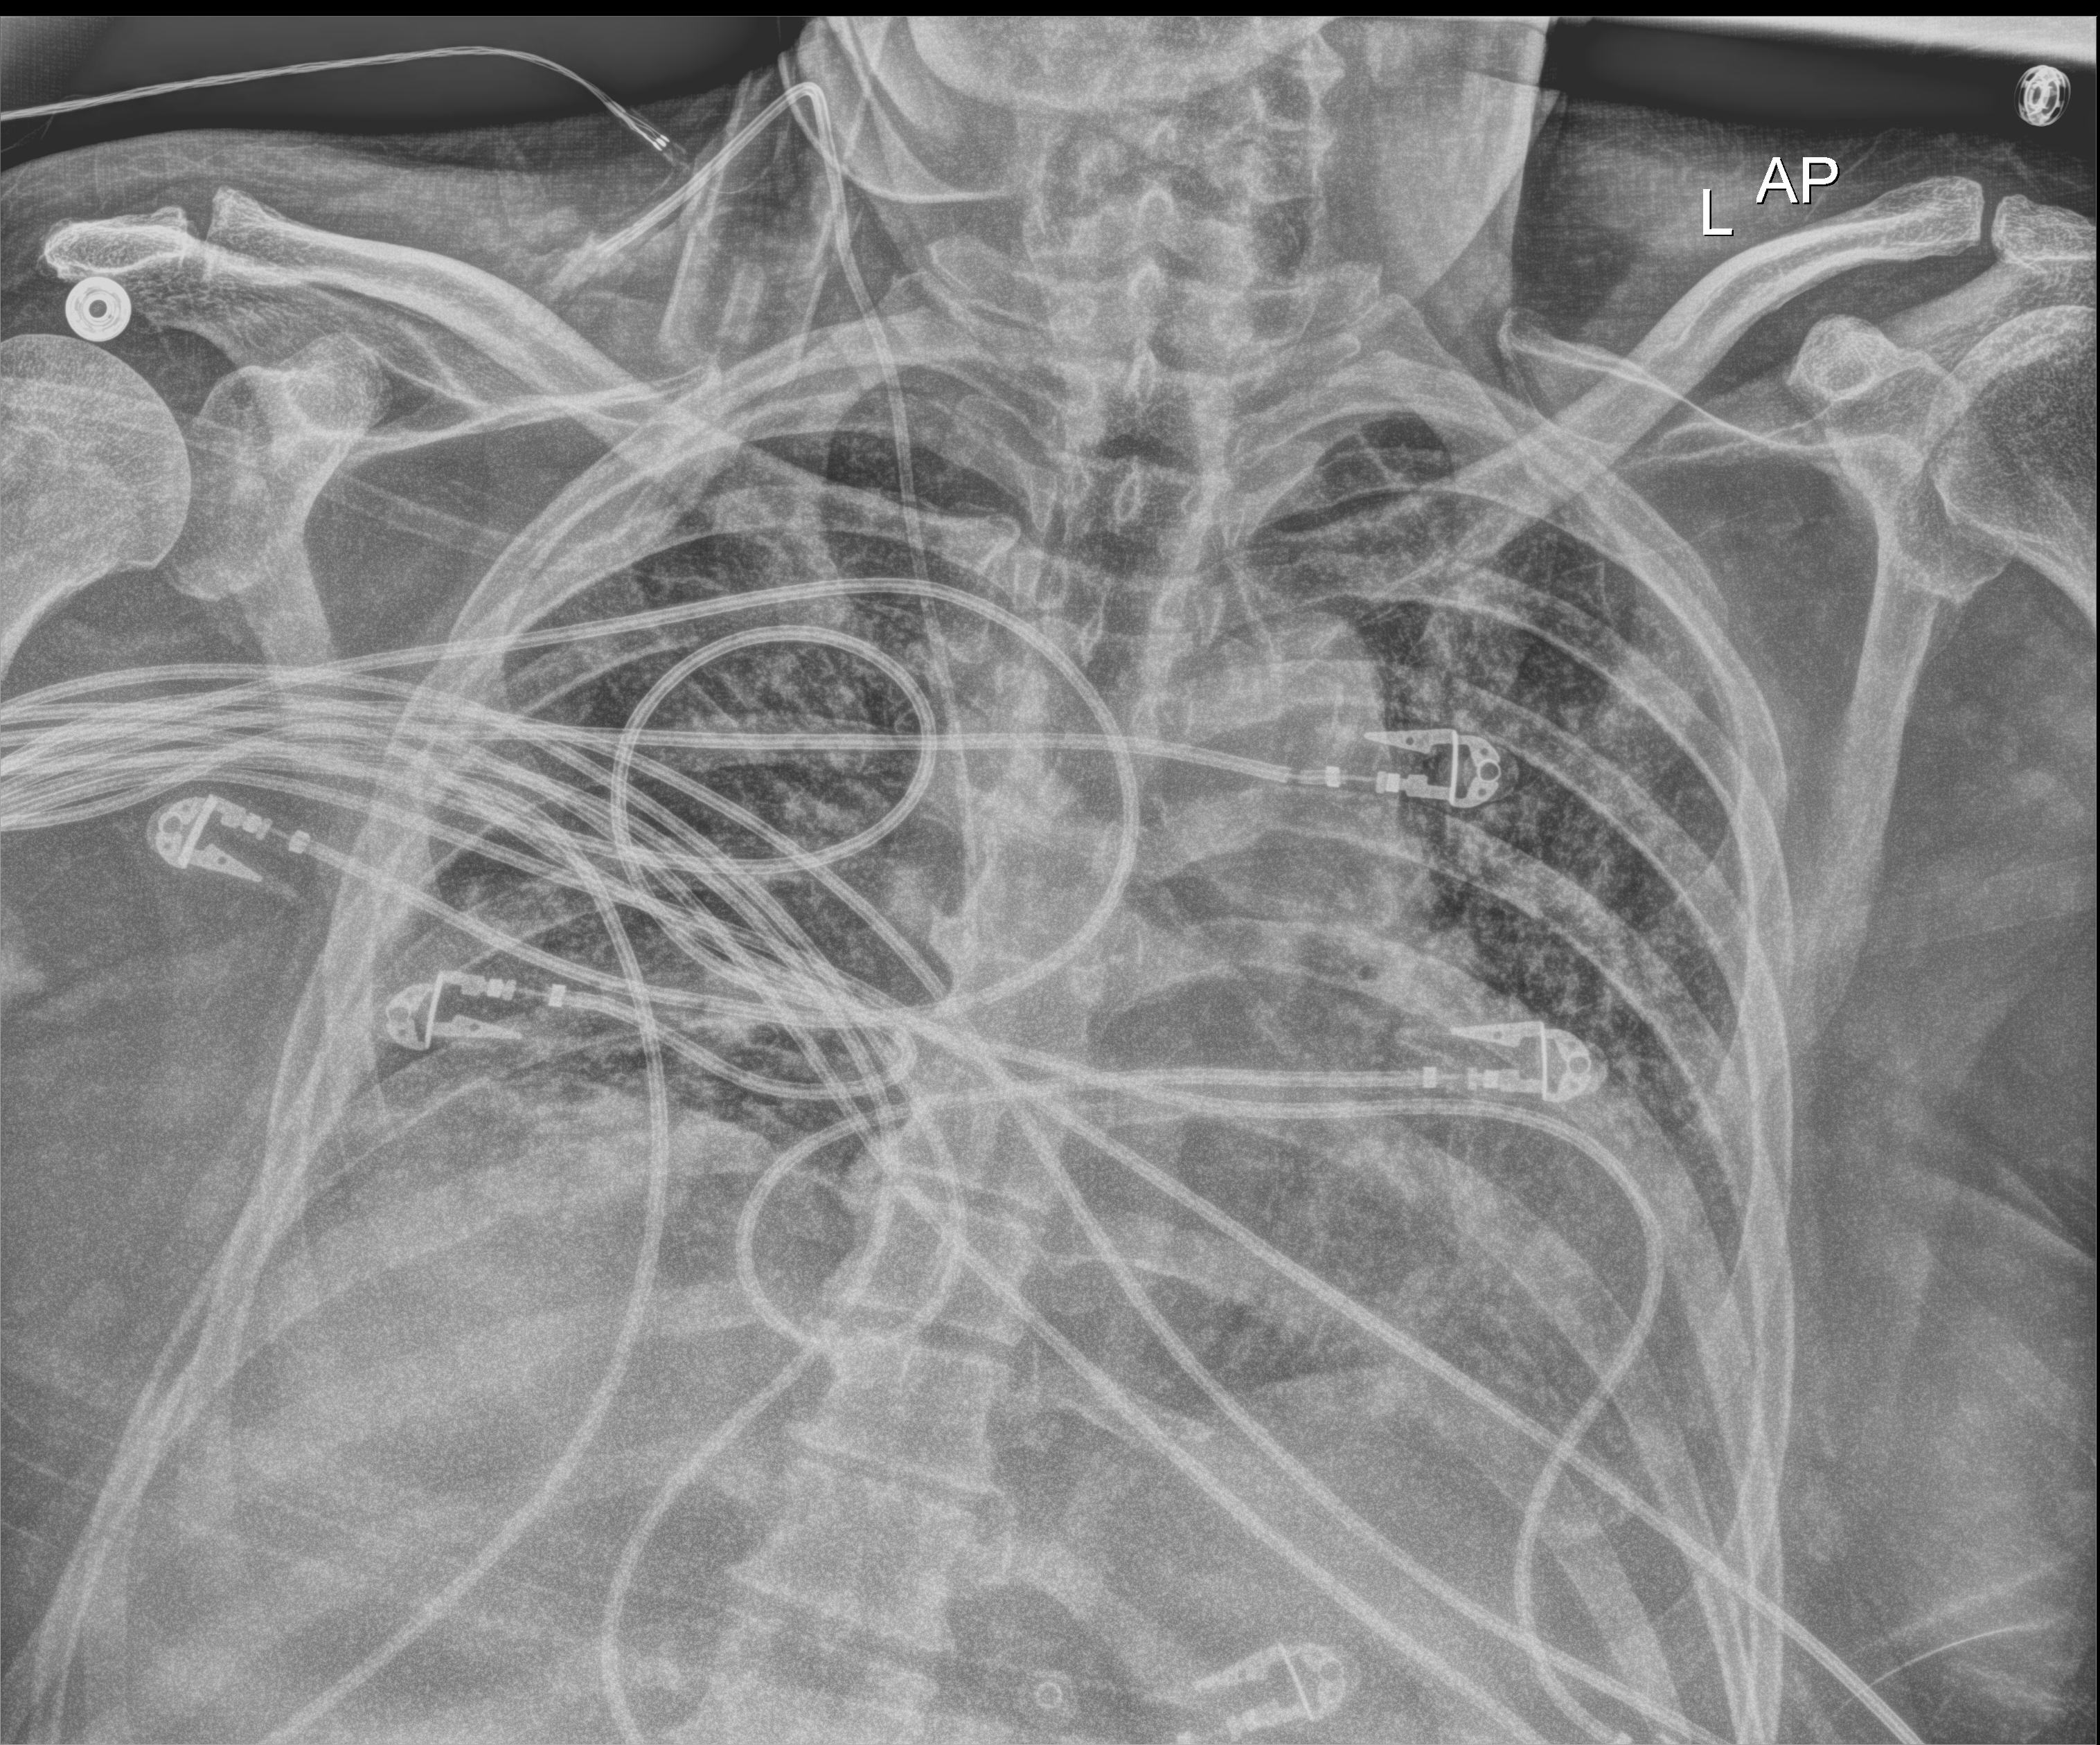
Portable chest radiograph; anteroposterior (AP) projection. Male patient hospitalised with COVID-19, age 60–74 years.
Admission-level facts for this patient (not findings on this image; timing relative to this image not recorded):
- admitted to intensive care during this hospital stay: yes
- hypertension (admission record): yes
- length of hospital stay: 40 days